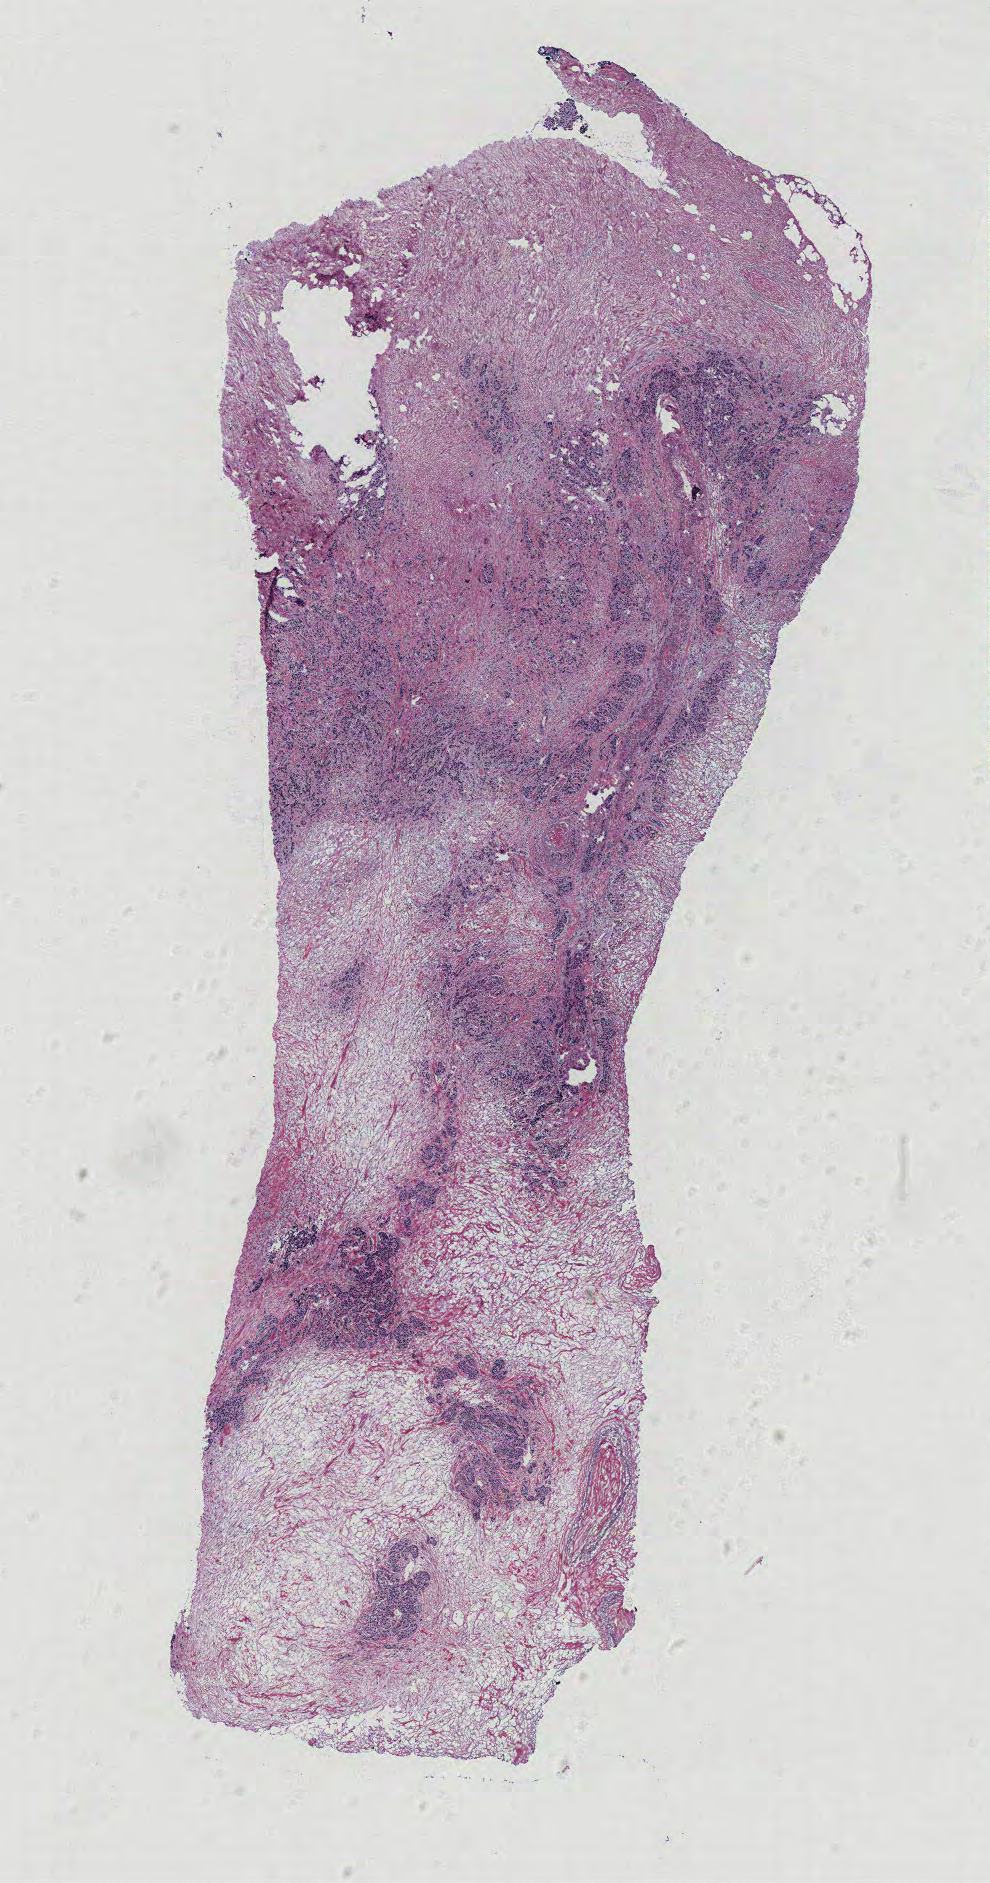
Digitized Hematoxylin and eosin (H&E) stained tissue section (whole slide) — a low-resolution overview of the entire scanned area, about 7.9 x 15.1 mm. Tumour tissue sample, breast. Female patient, aged 90 or older.
• diagnosis: Infiltrating duct carcinoma, NOS
• AJCC pathologic stage: IIA